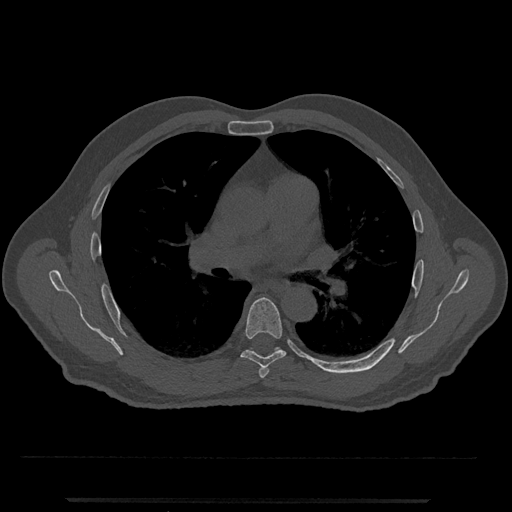
CT including the spine, one axial slice. Slice 734 of 797 in the series (ordered by position). Reconstruction kernel Br40s/3. 120 kVp. Bone window (W 1800 / L 400 HU). 512 × 512 image matrix, field of view 419 × 419 mm. Patient: male, 63 years. Case-level facts recorded for this patient, not image findings: primary cancer: prostate.
Annotated regions visible in this slice (semi-automatically segmented with operator editing):
- T5 vertebra: bounding box [x1, y1, x2, y2] px = [259, 366, 269, 378]
- T6 vertebra: [241, 297, 286, 368]
- T7 vertebra: [251, 347, 280, 350]